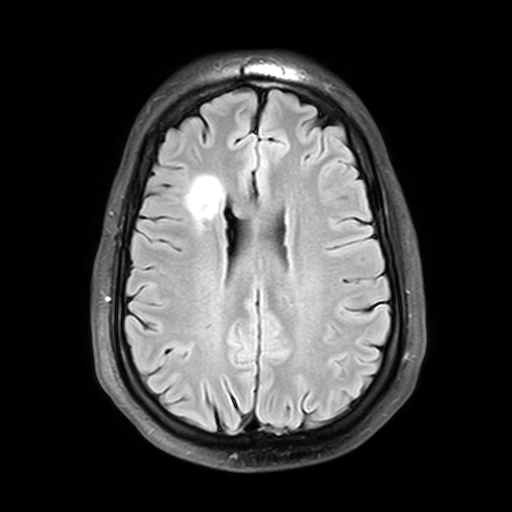
Brain MRI from a brain-tumour surgery series, one axial slice. Slice 15 of 42 in the series (ordered by position). T2 FLAIR. 4 mm slice thickness. 512 × 512 image matrix. Case-level facts recorded for this patient, not image findings: histopathology: Astrocytoma; WHO grade: 2; IDH mutation: yes.
Outlined on this slice (outlined manually by an expert reader):
- tumour: bounding box (x1, y1, x2, y2) in pixels: (185, 176, 223, 218)